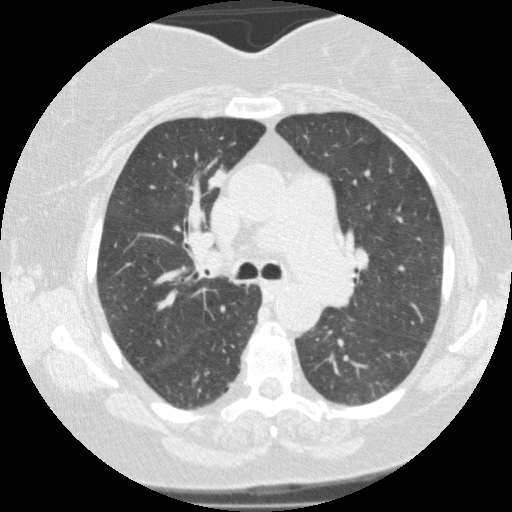
Low-dose screening chest CT, one axial slice. Lung window (W 1500 / L -600 HU). 2 mm slice thickness. 512 × 512 image matrix.
Annotated regions visible in this slice (manually delineated by an expert):
- lesion 2 (tumor, upper lobe of right lung): bounding box (x1, y1, x2, y2) in pixels: (206, 170, 227, 189)